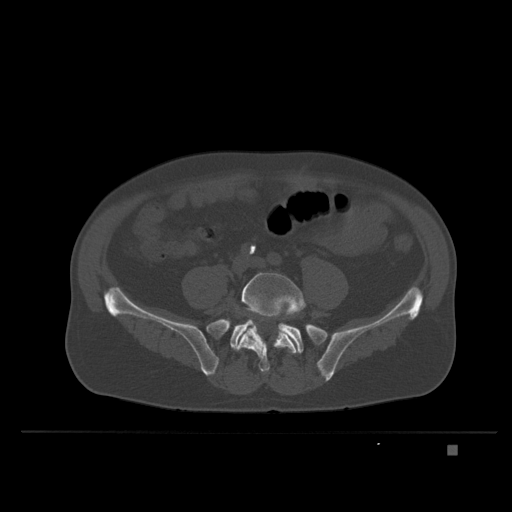
CT including the spine, one axial slice. Slice 52 of 435 in the series (ordered by position). Bone window (W 1800 / L 400 HU). 1.5 mm slice thickness. 512 × 512 image matrix. Patient: male, 73 years. From the clinical record (not read from this slice): primary cancer: skin.
Outlined on this slice (semi-automatically segmented with operator editing):
- L5 vertebra: bounding box [x1, y1, x2, y2] px = [238, 272, 304, 375]